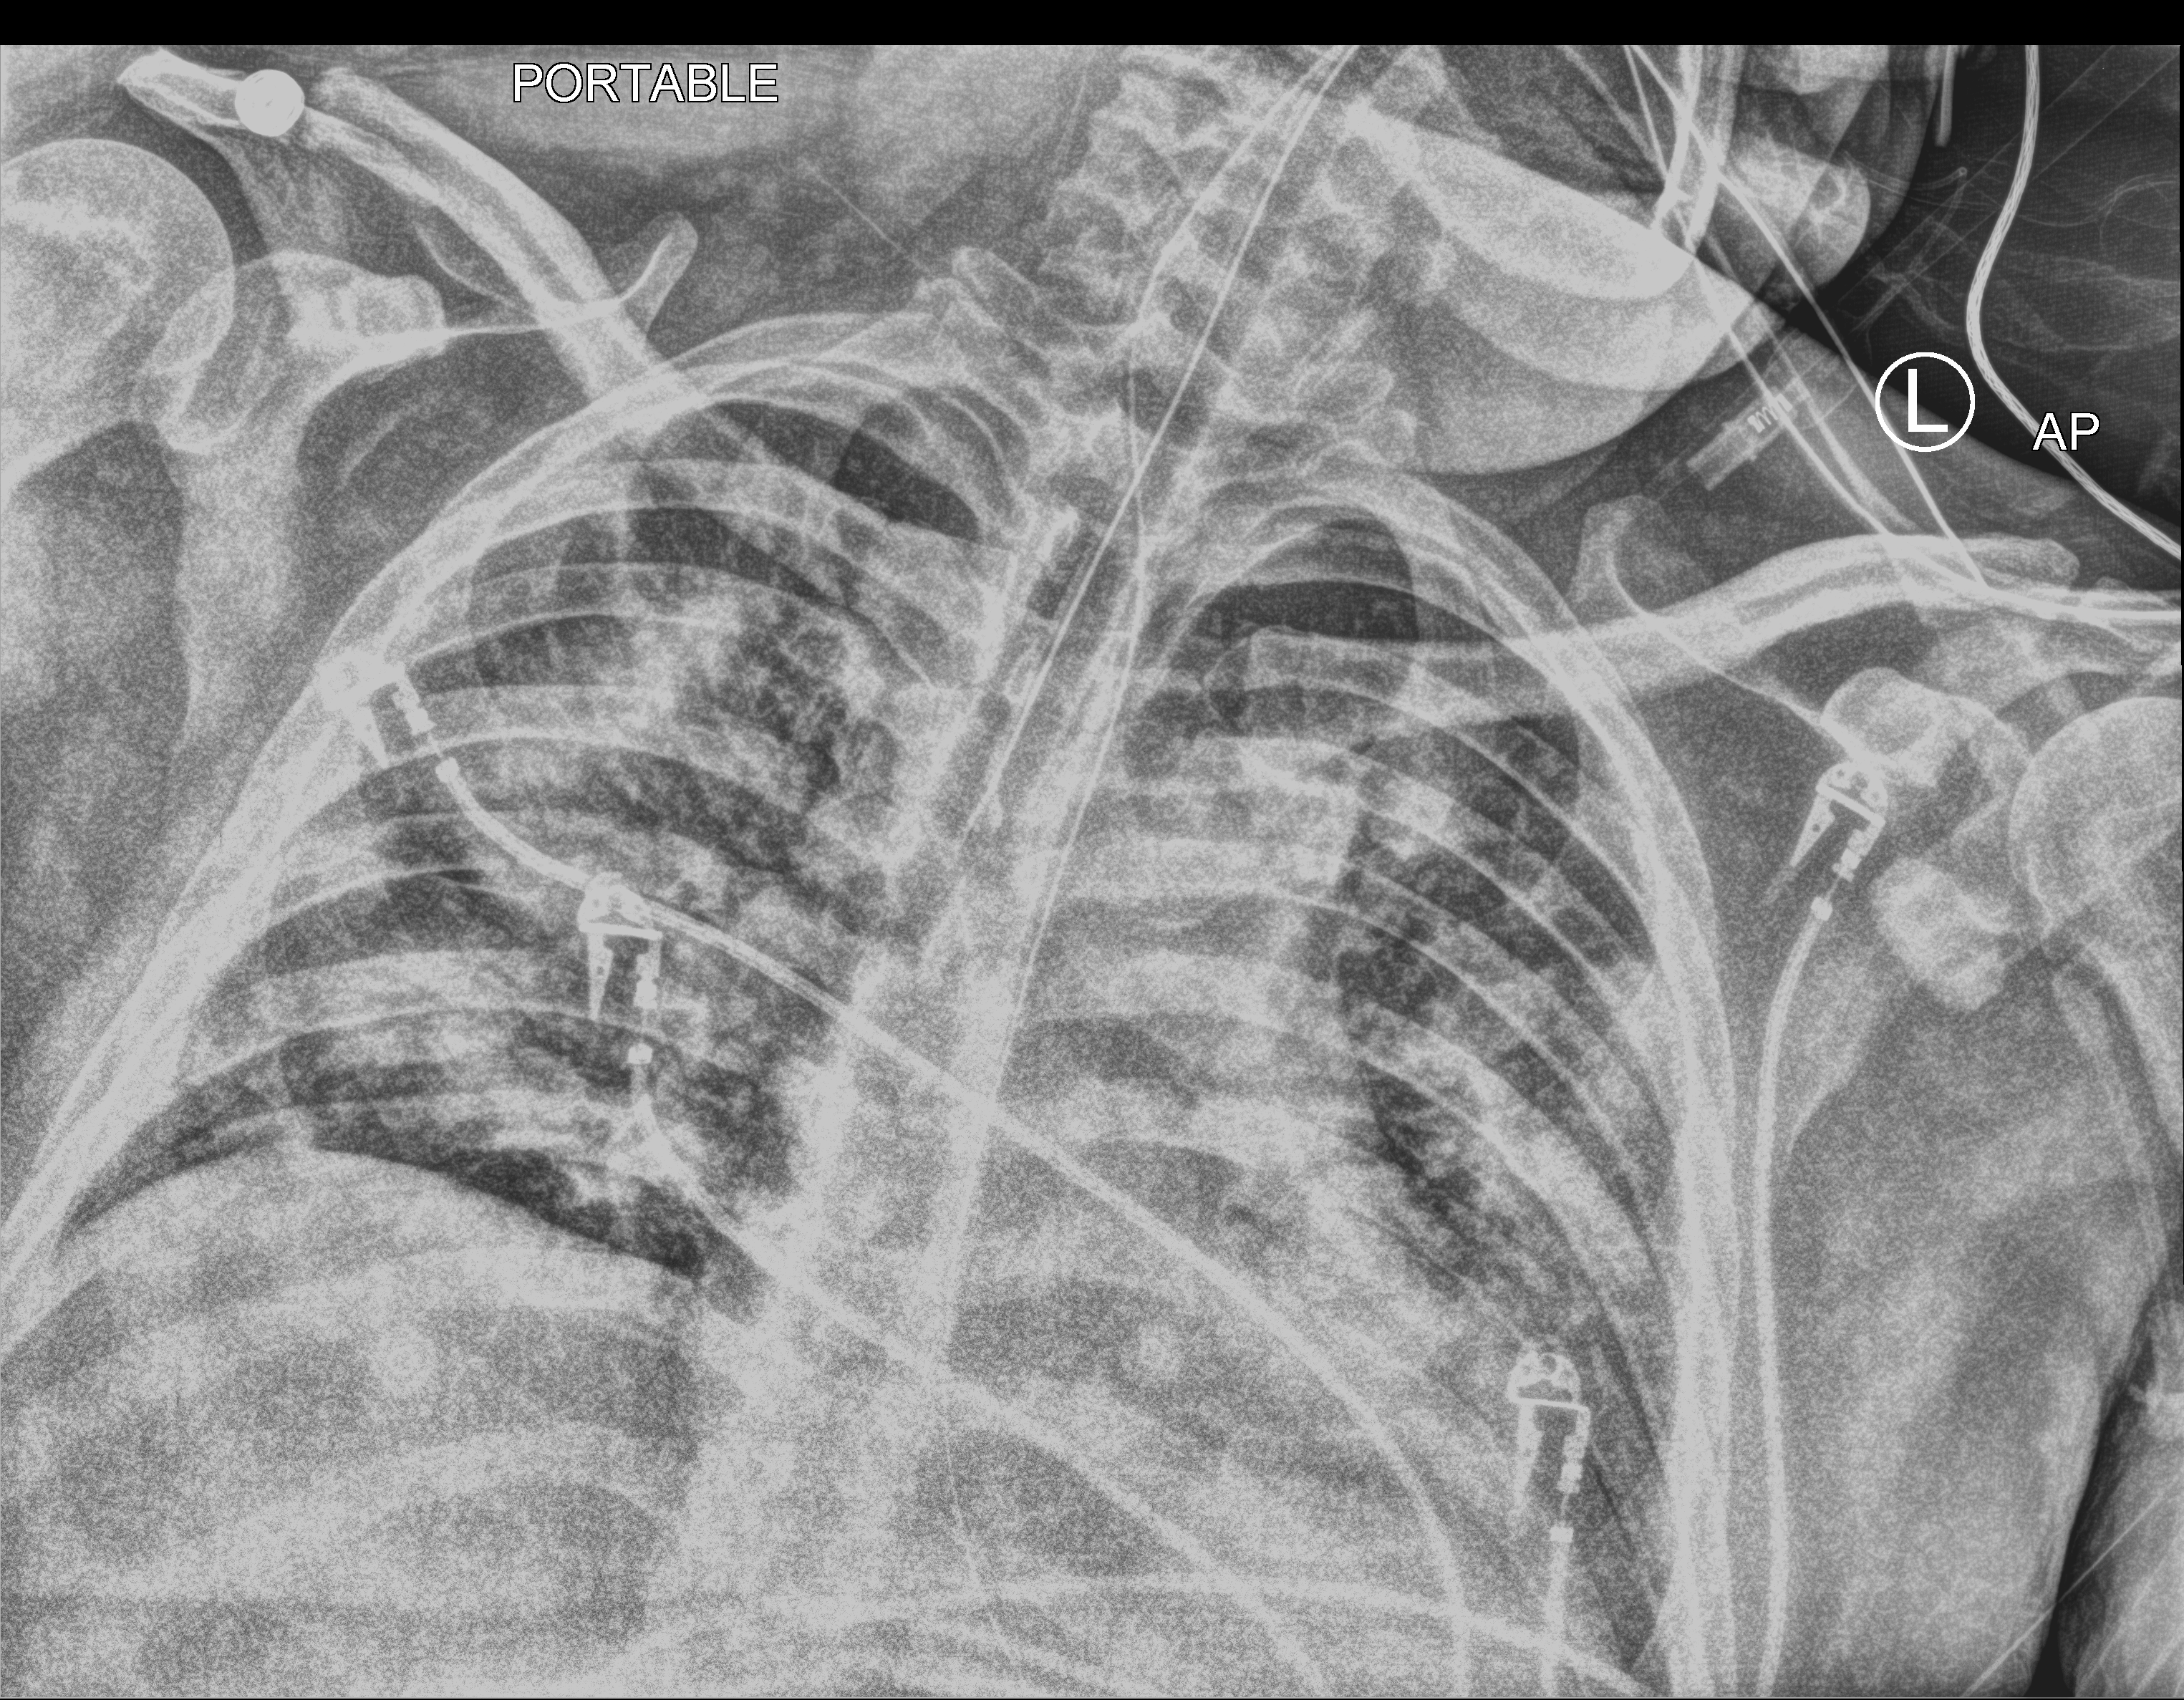
Portable chest radiograph; anteroposterior (AP) projection. Patient hospitalised with COVID-19; male, aged 18–59 years.
Hospital-stay facts (about this admission, not read from this image; timing relative to this image not recorded):
- length of hospital stay: 30 days